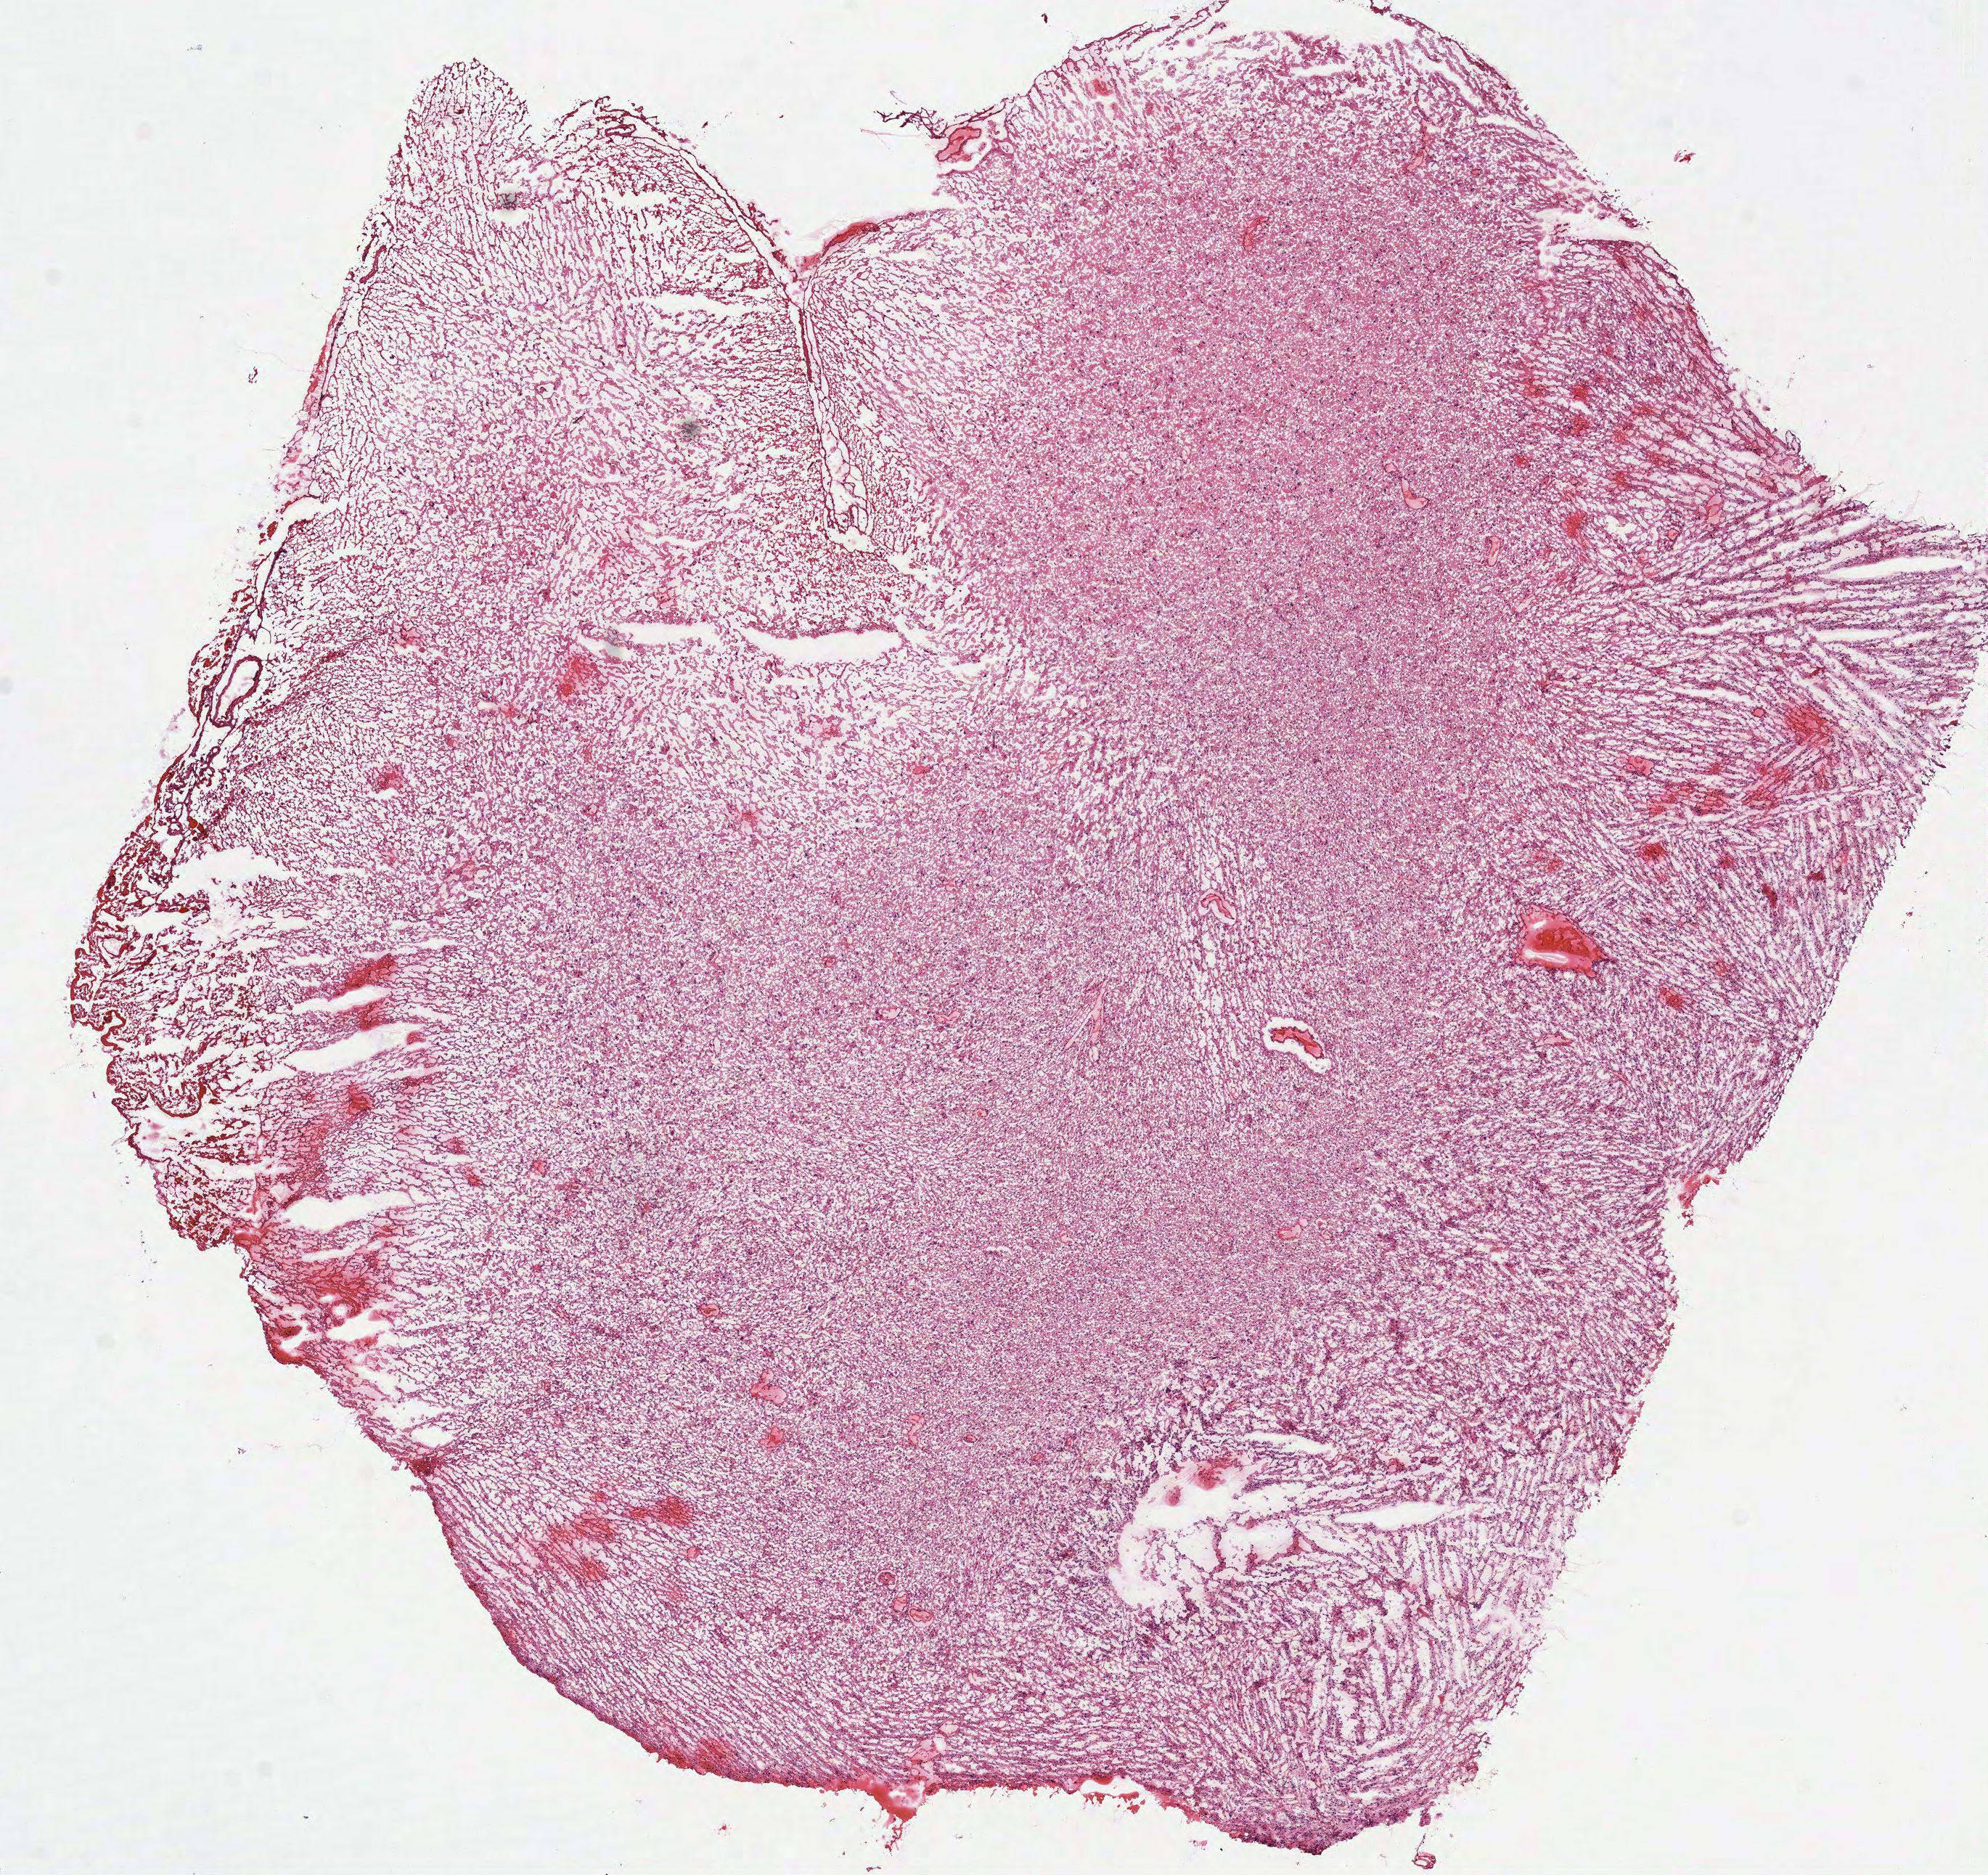
Digitized H&E-stained tissue section (whole slide), shown as a low-resolution overview of the whole scanned area (about 11.0 x 10.4 mm, from a 40x scan), frozen section, brain, primary tumour sample. Patient: female, age at initial diagnosis 44 years. Slide review estimates, as recorded: tumour cells 100%, tumour nuclei 70%, normal cells 0%, stromal cells 0%, necrosis 0%.
Pathologic diagnosis: Glioblastoma.